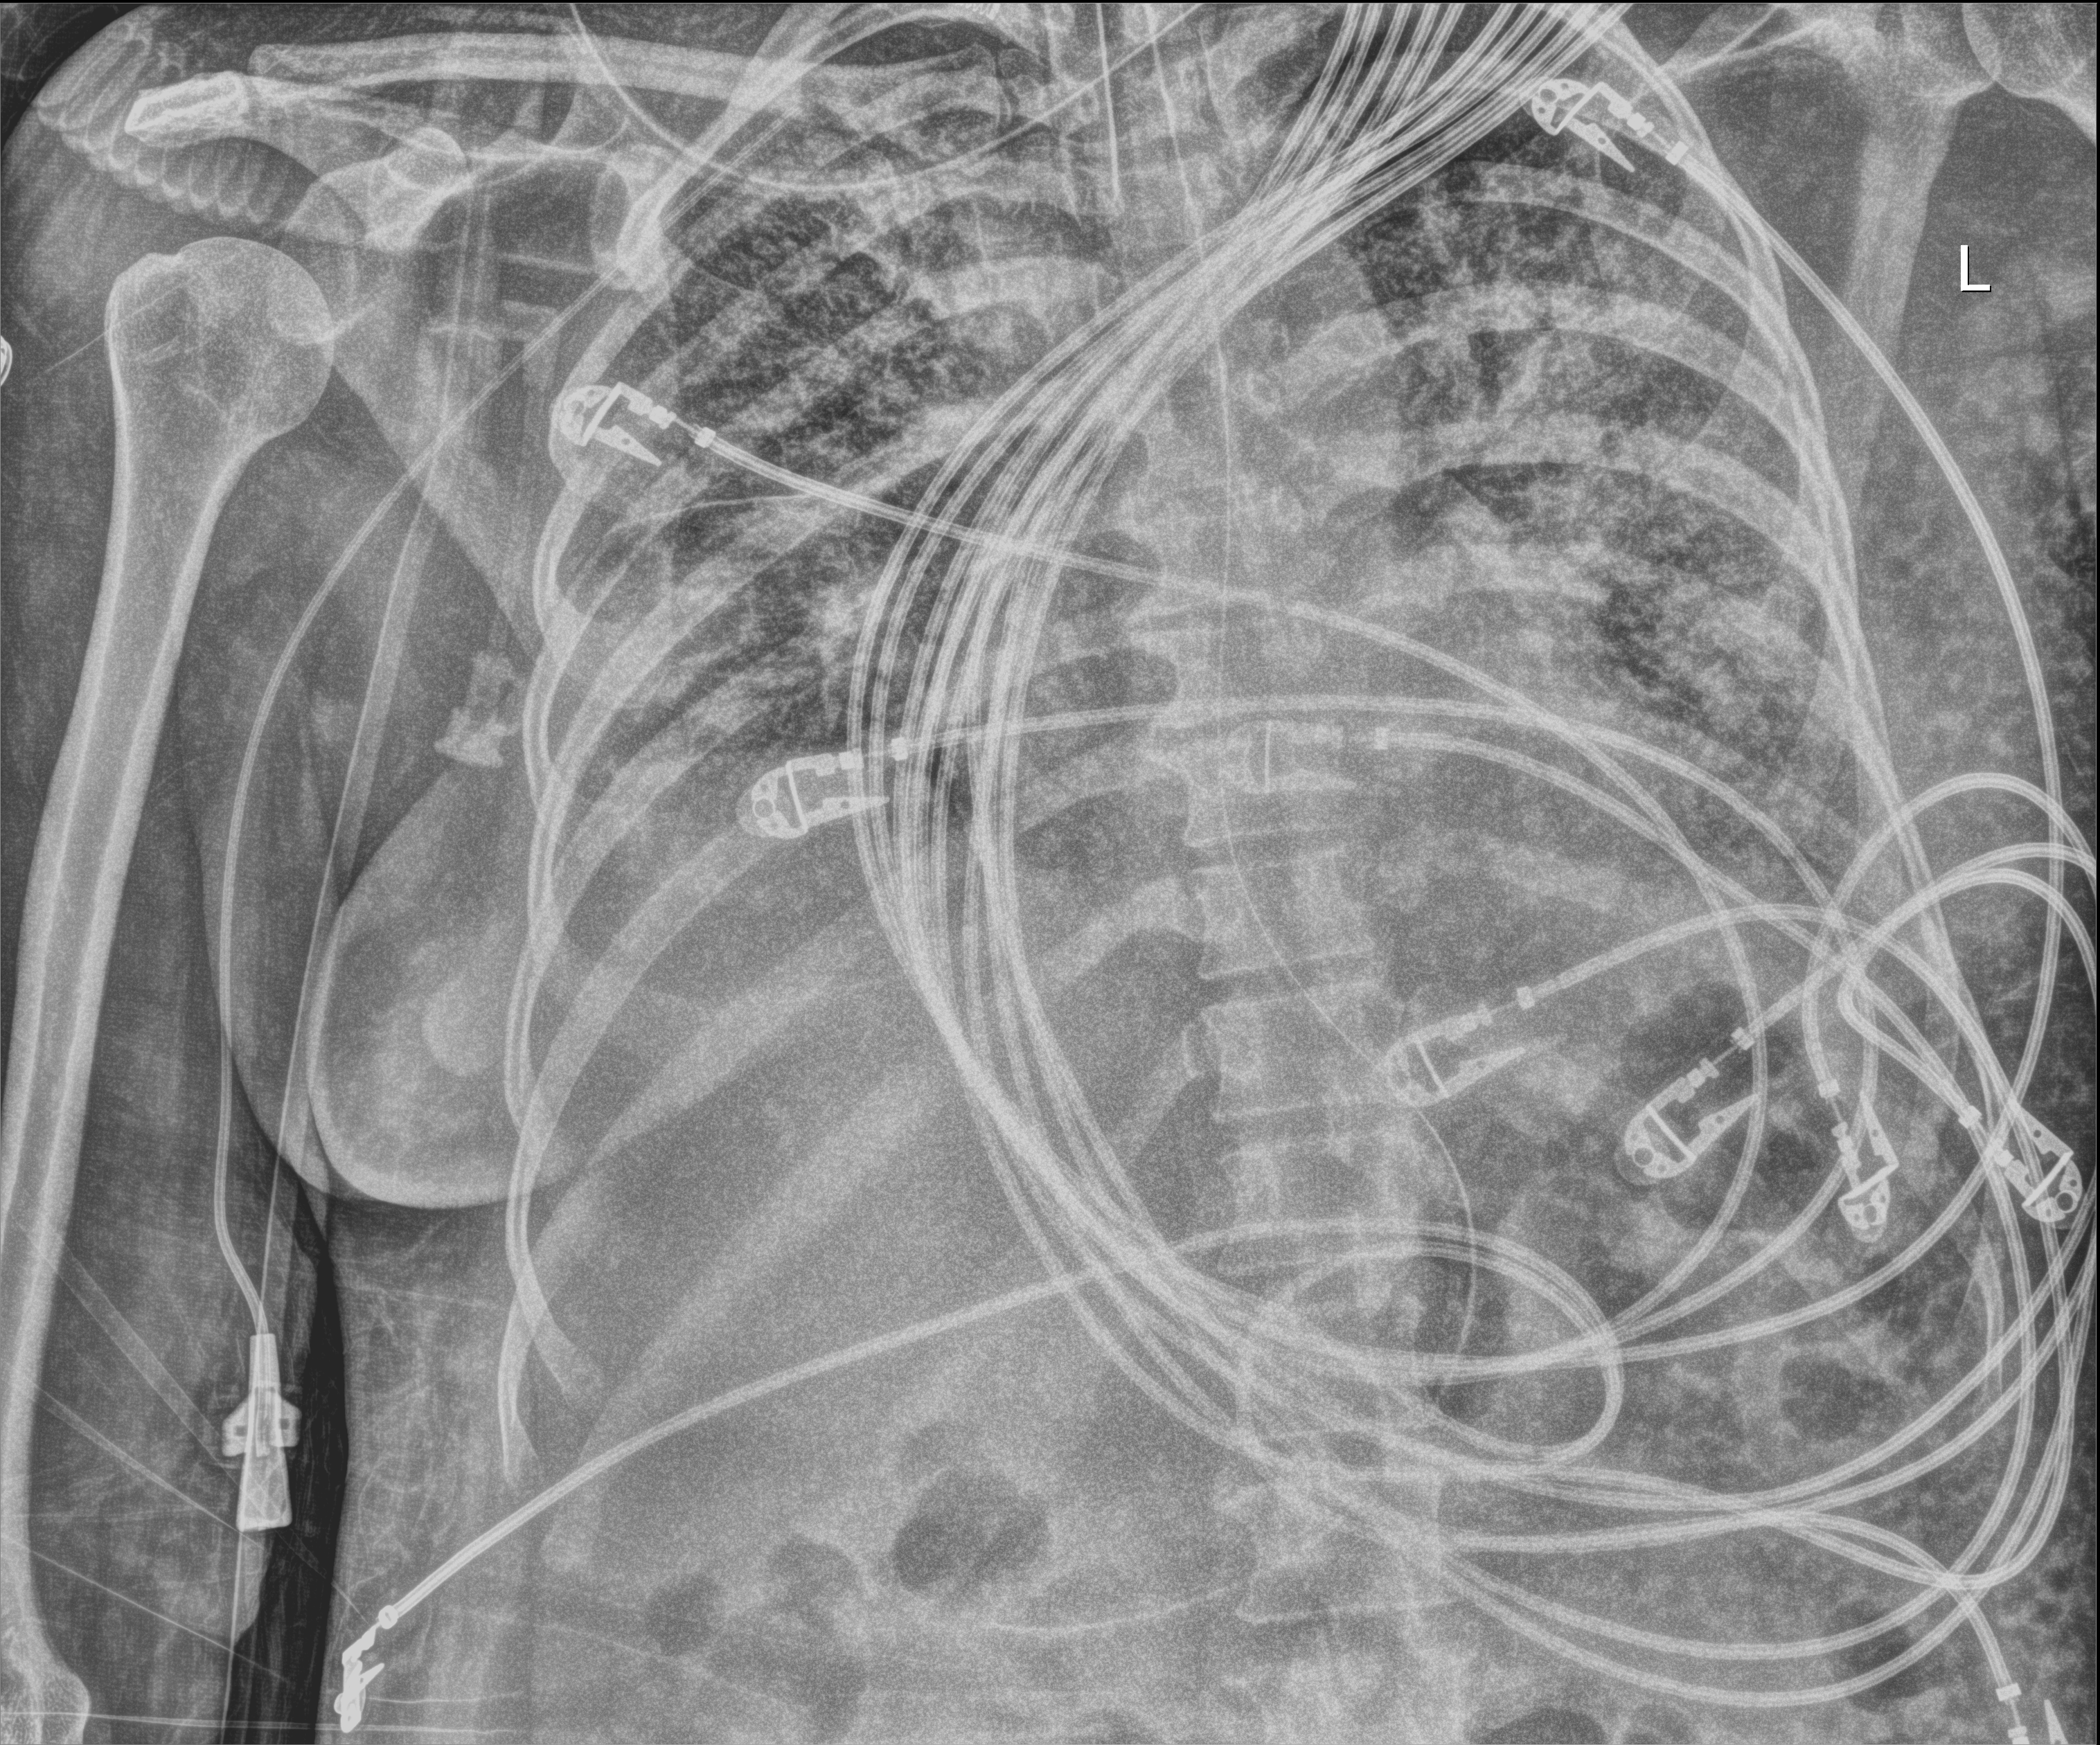
Chest radiograph; anteroposterior (AP) projection. Patient hospitalised with COVID-19; female, aged 18–59 years.
Hospital-stay facts (about this admission, not read from this image; timing relative to this image not recorded):
- mechanically ventilated during this hospital stay: yes
- length of hospital stay: 71 days